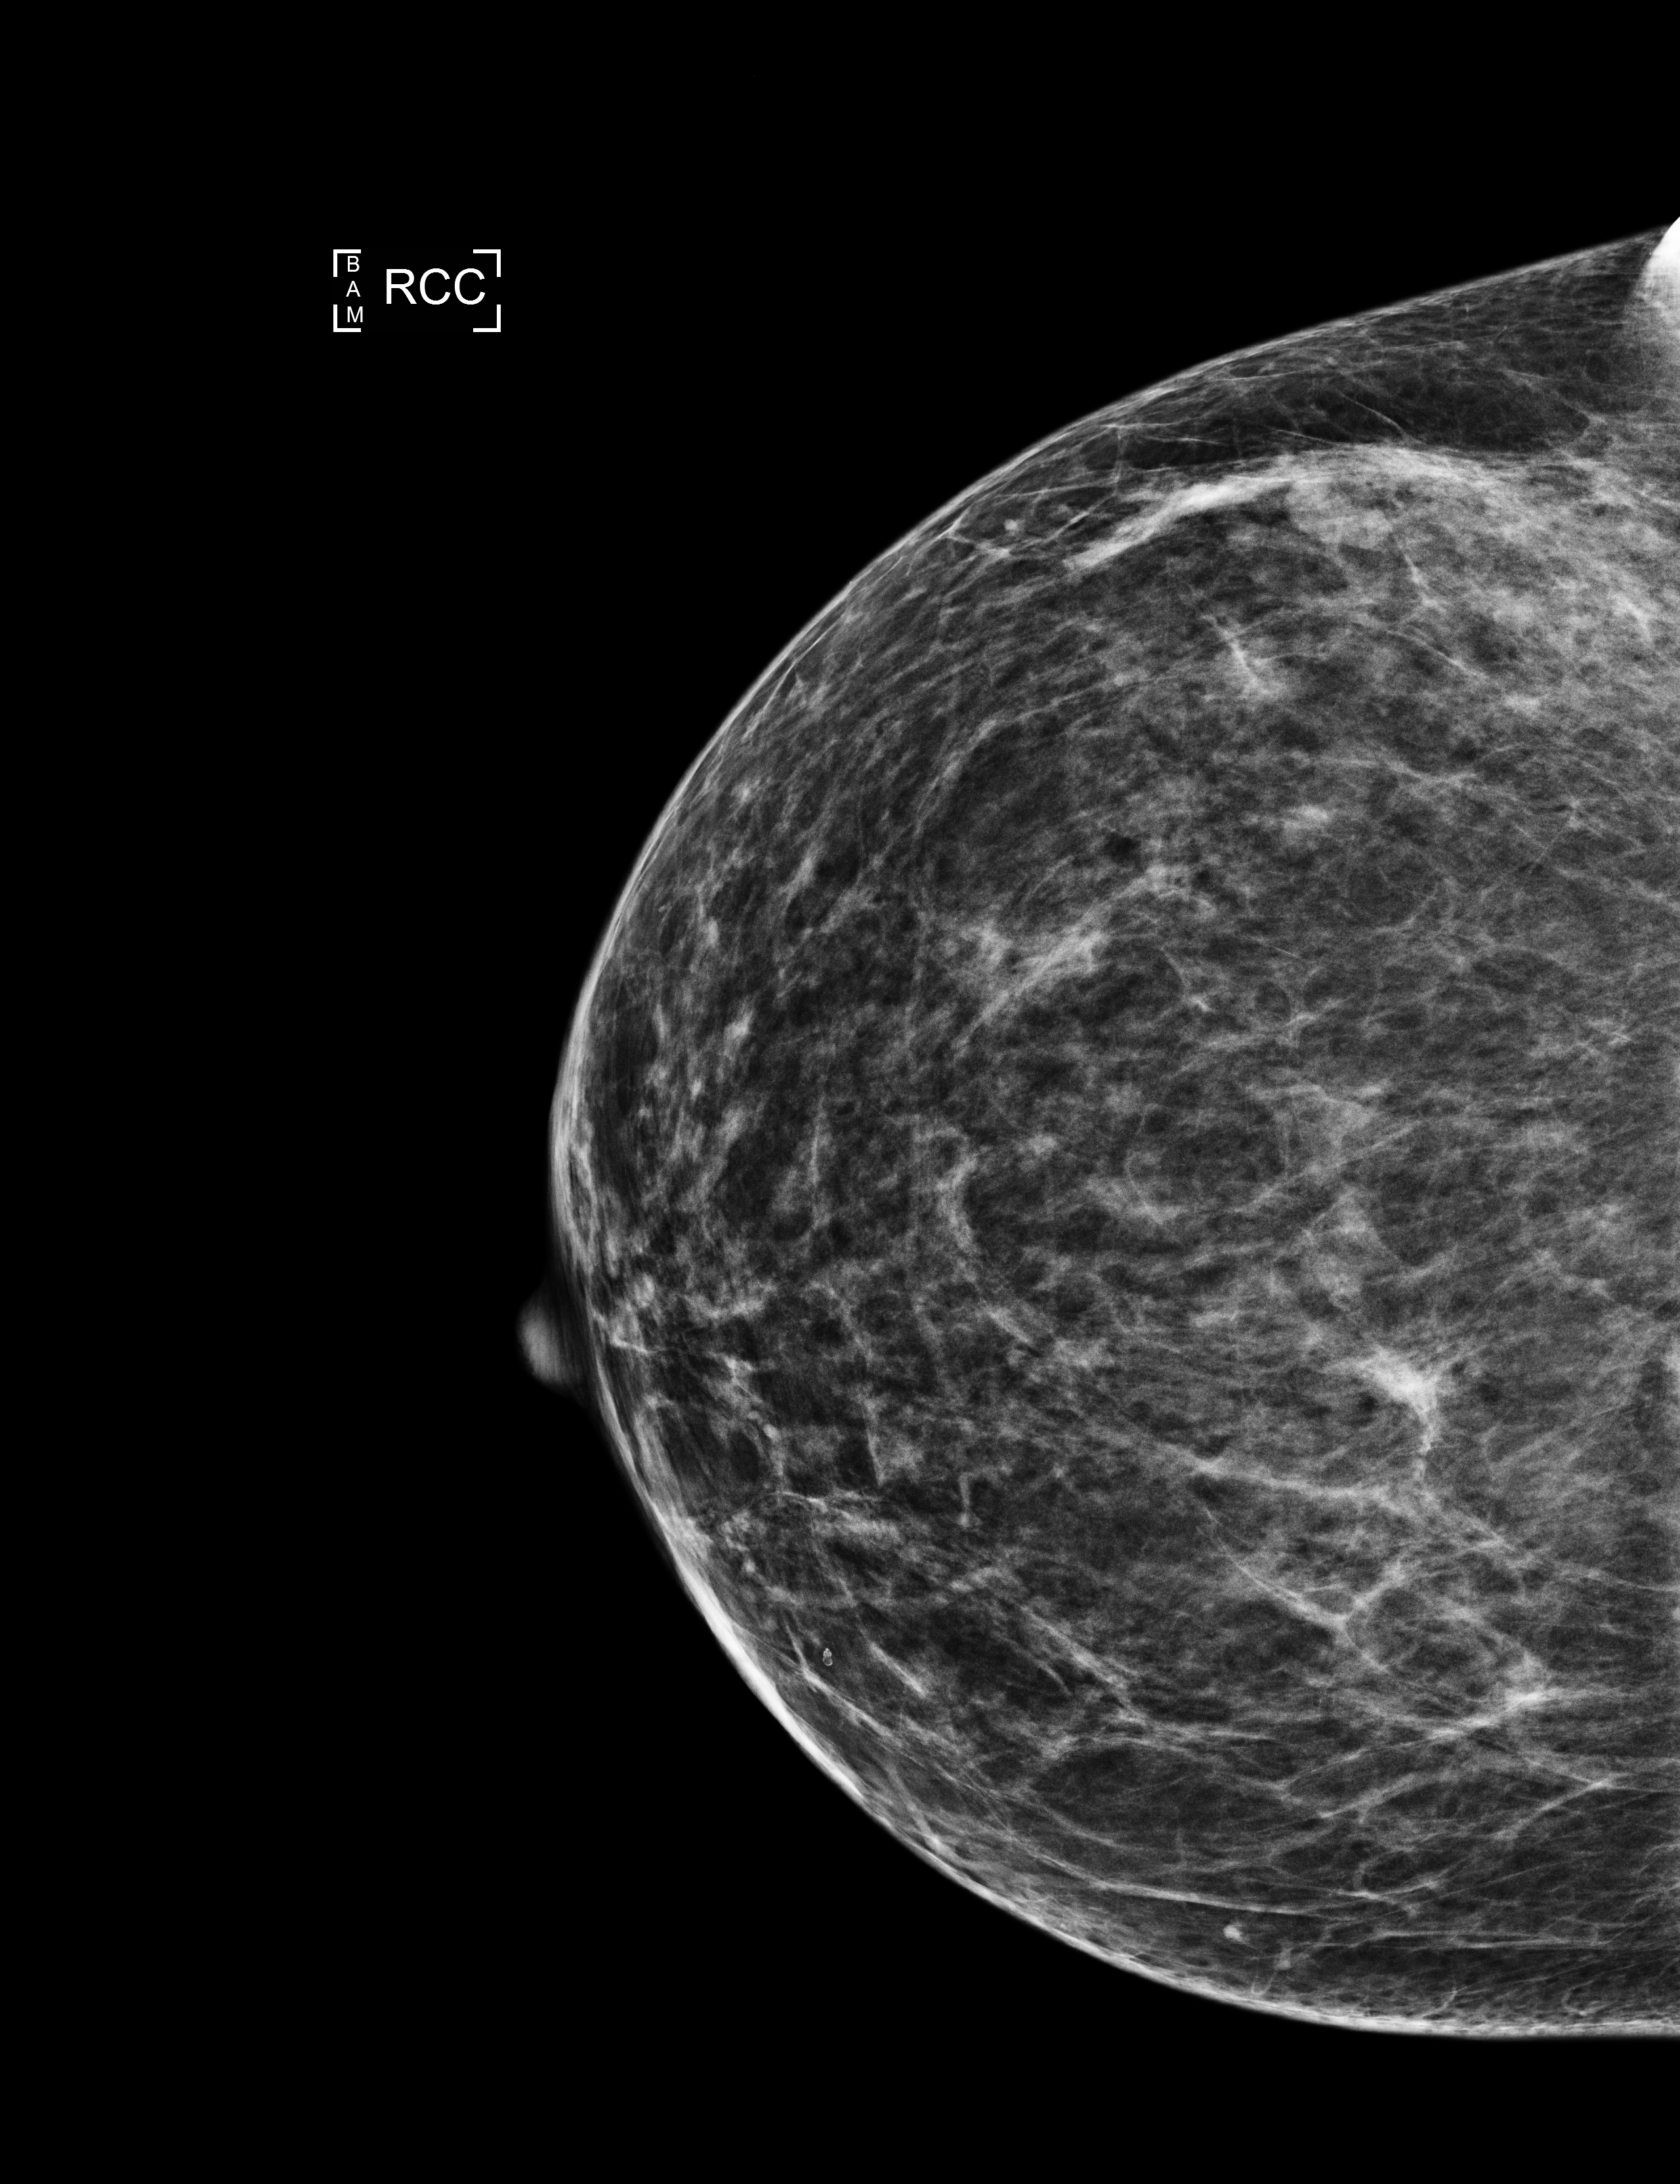
Annual screening mammography examination, compressed breast thickness 56 mm. Female patient, age 45 years.
Image type: full-field digital mammogram. Breast: right. Projection: craniocaudal (CC) view.